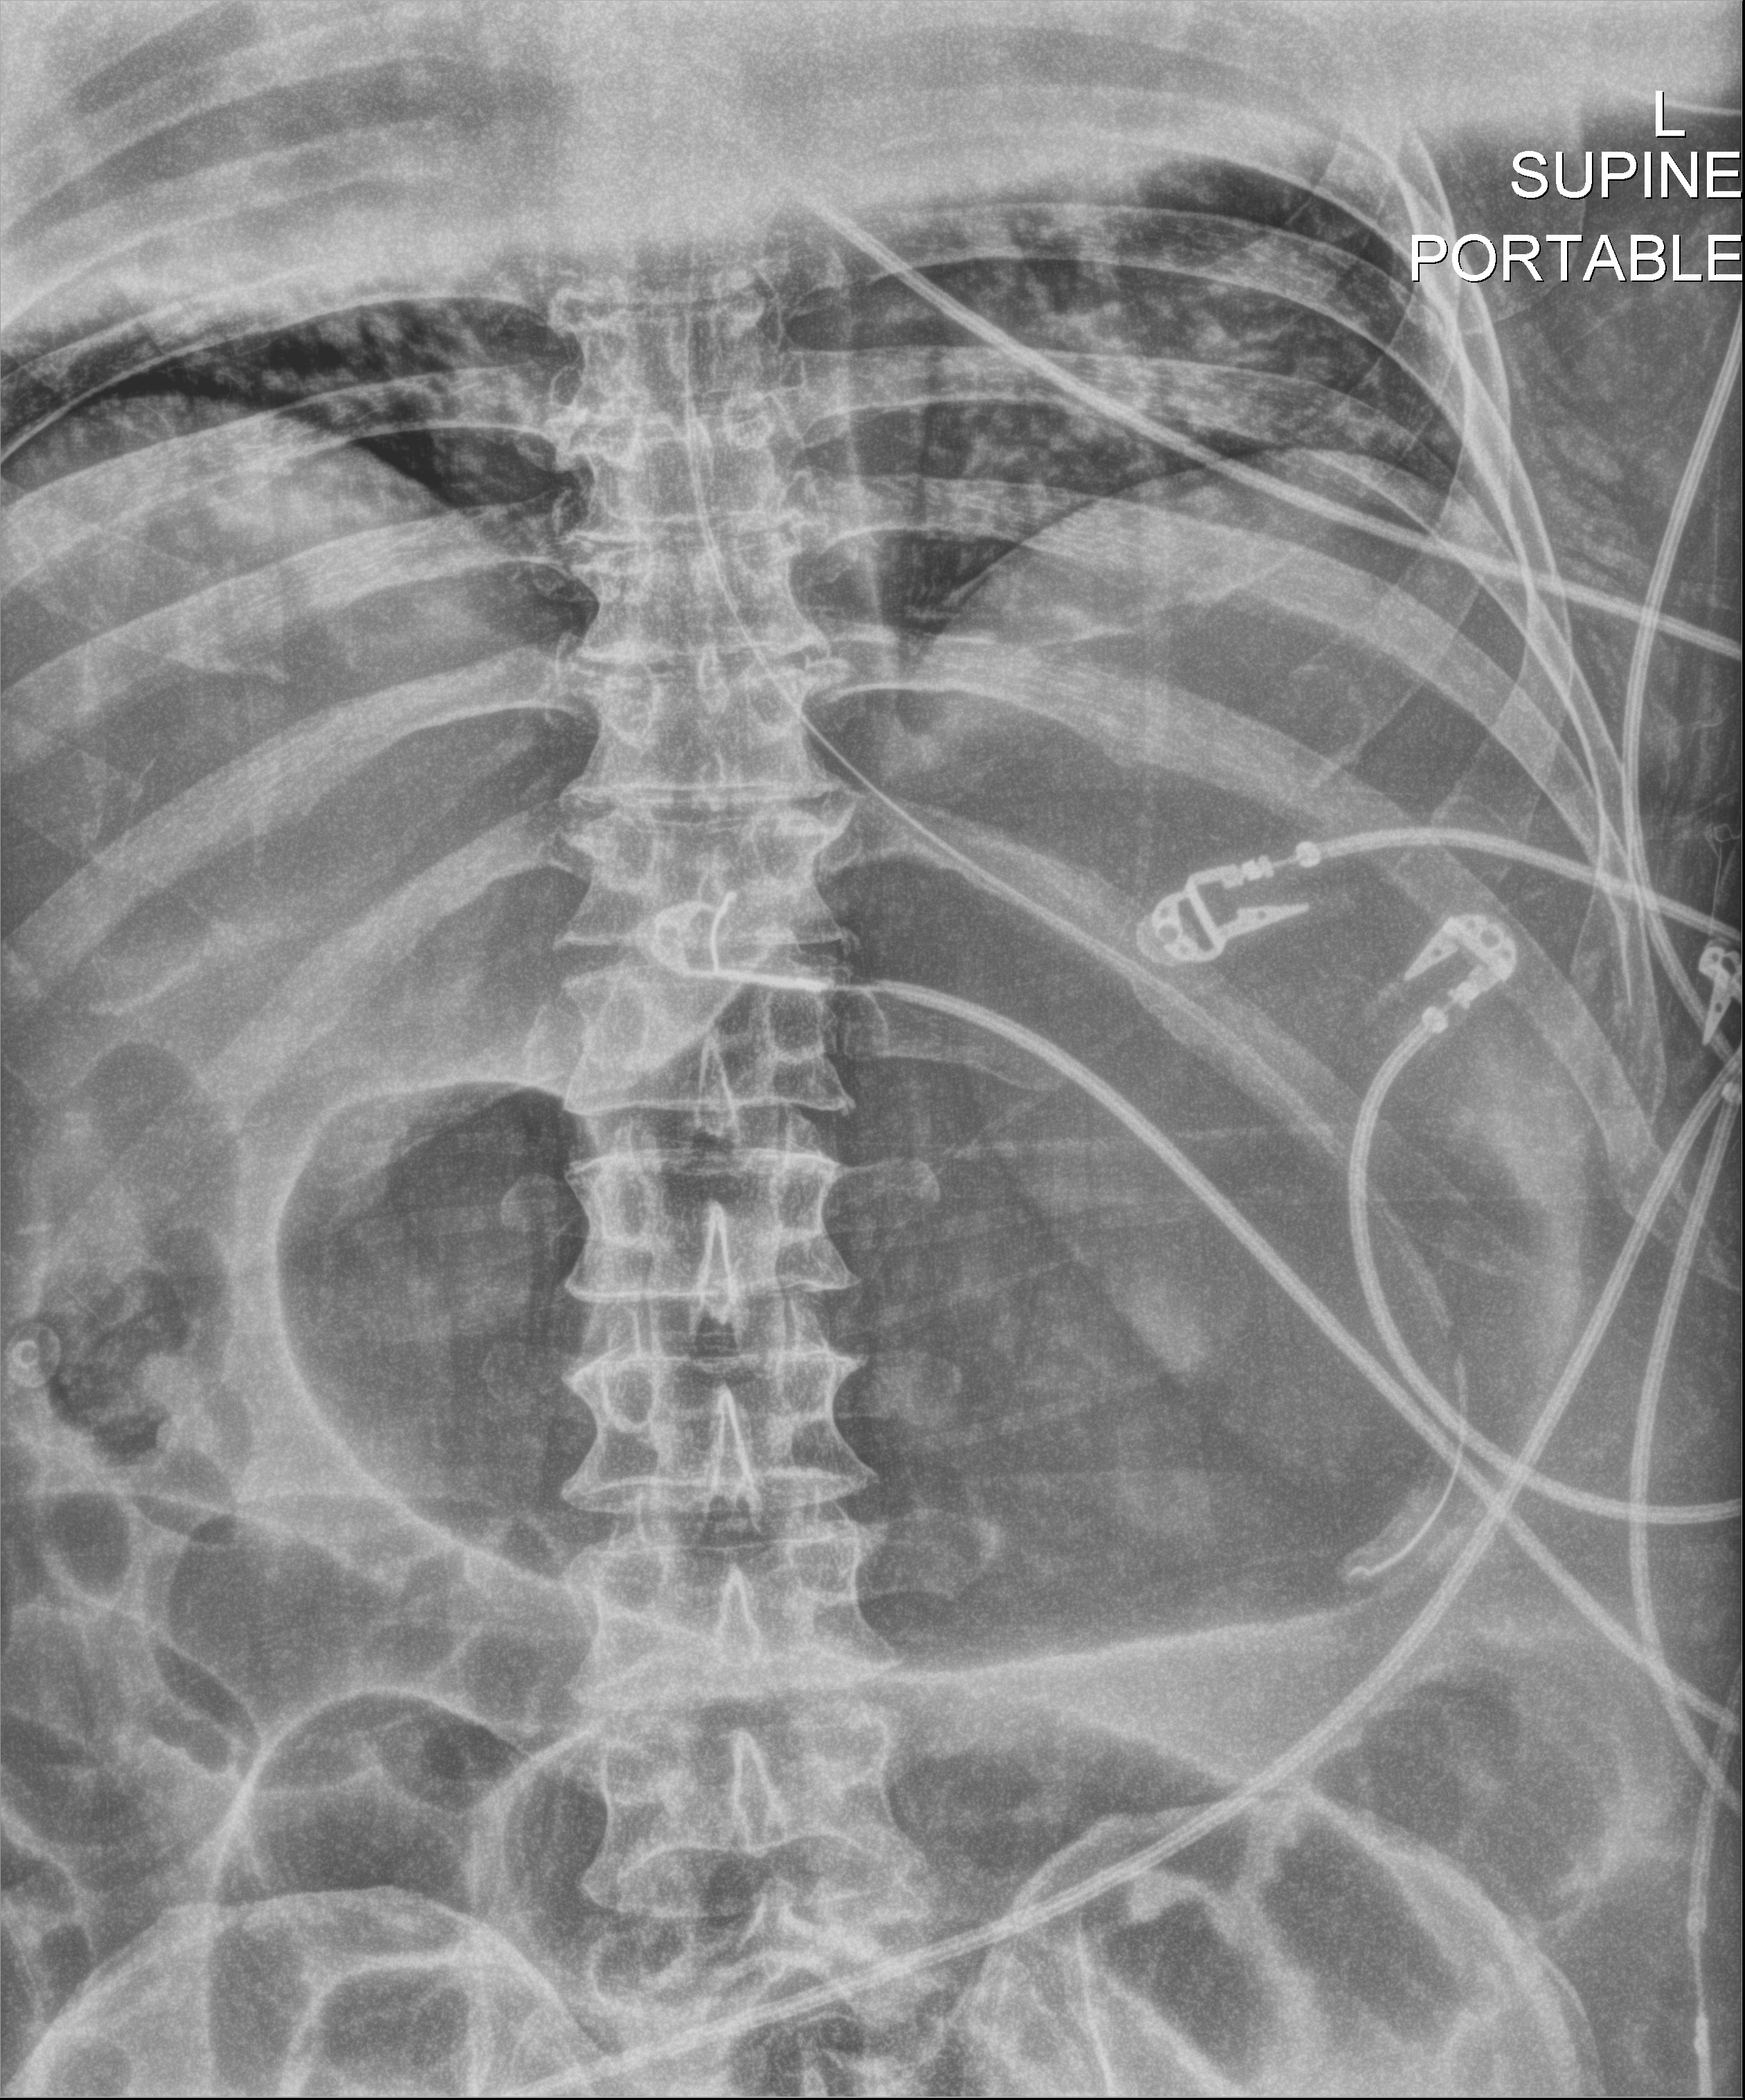
Portable abdomen radiograph; anteroposterior (AP) projection. Male patient hospitalised with COVID-19, age 18–59 years.
Admission-level facts for this patient (not findings on this image; timing relative to this image not recorded): mechanically ventilated during this hospital stay: yes; admitted to intensive care during this hospital stay: yes.